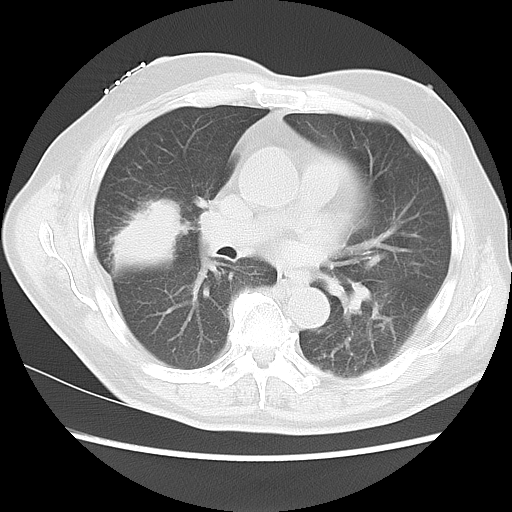
Chest CT, one axial slice. Slice 4 of 15 in the series (ordered by position). Reconstruction kernel LUNG. Lung window (W 1500 / L -600 HU). 5 mm slice thickness. 512 × 512 image matrix, field of view 350 × 350 mm. Patient: male, 68 years. From the clinical record (not read from this slice): clinical TNM (as recorded): T4 N3 M0.
Structures marked on this image (bounding box drawn by a radiologist):
- lung tumour (recorded histology: squamous cell carcinoma): bounding box <110,189,184,276> (left, top, right, bottom; pixels)